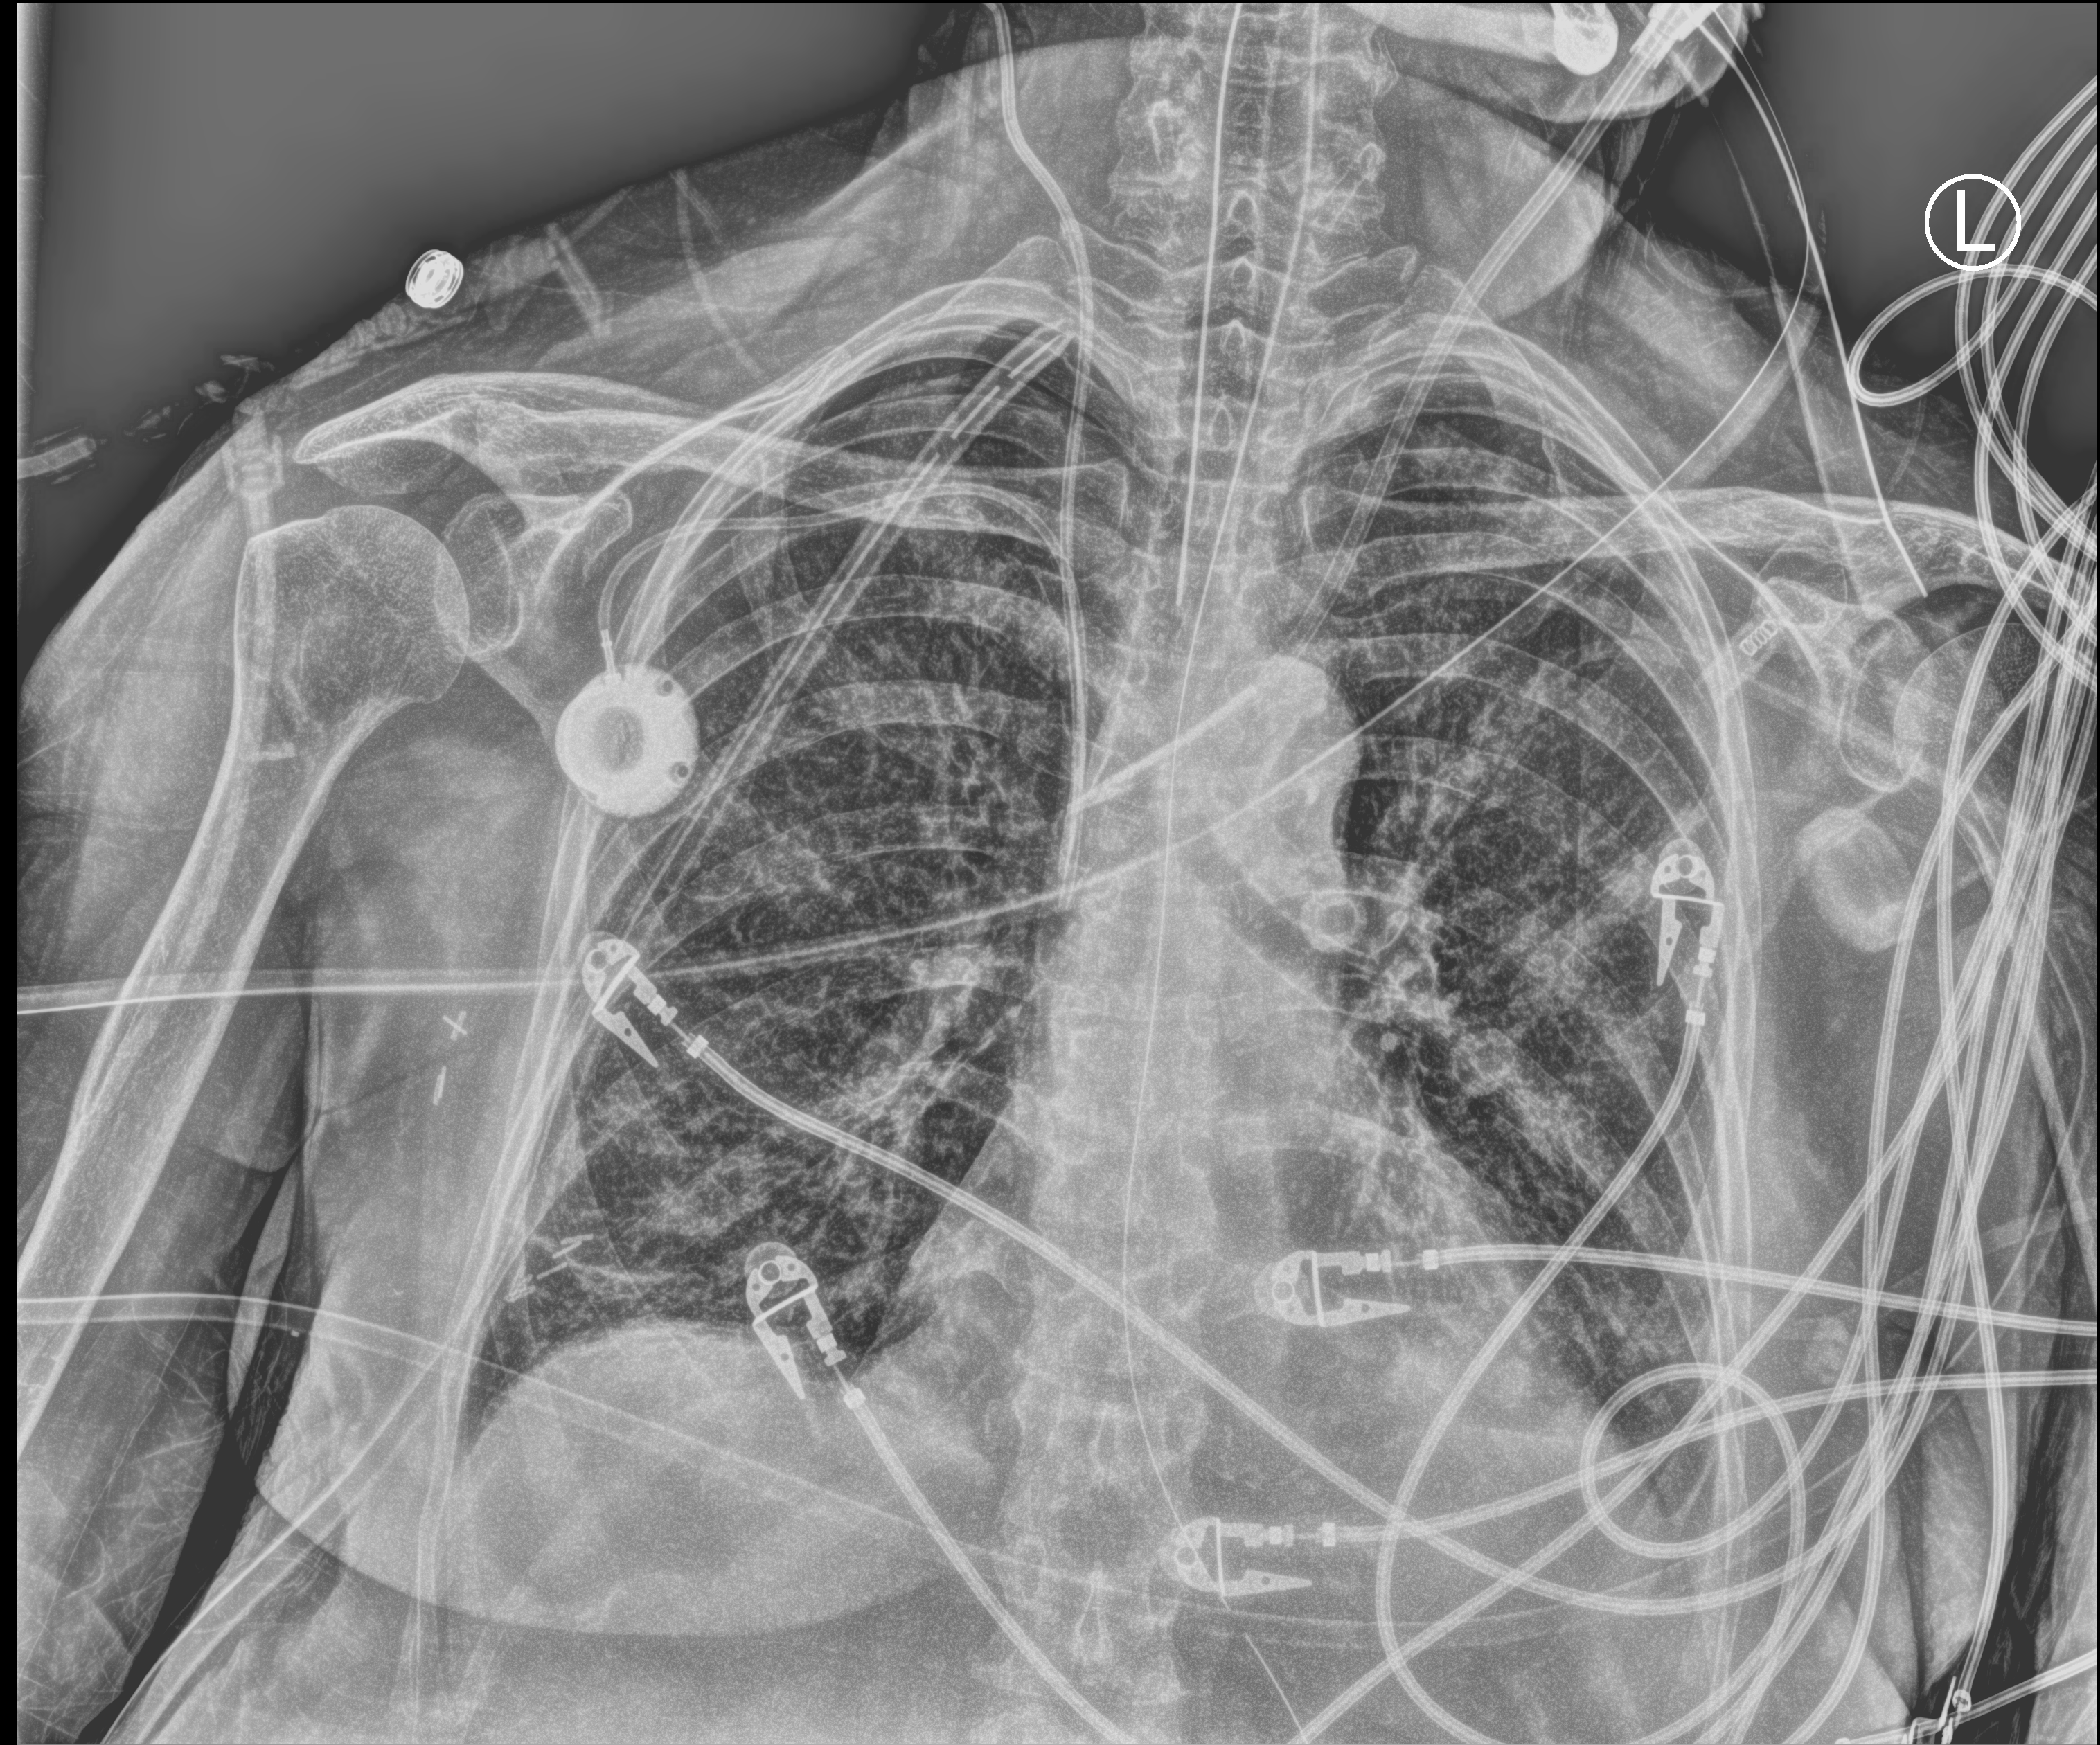
Bedside chest radiograph (computed radiography); anteroposterior (AP) projection. Female patient hospitalised with COVID-19, age 60–74 years.
Hospital-stay facts (about this admission, not read from this image; timing relative to this image not recorded):
- hypertension (admission record): yes
- other chronic lung disease (admission record): no
- length of hospital stay: 43 days